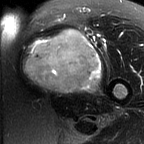
MRI of an extremity soft-tissue mass, one axial slice. T2-weighted fat-saturated. MR volume resampled by the dataset authors to the PET/CT grid (not the native acquisition matrix). 3.27 mm slice thickness. 144 × 144 image matrix. Female patient. From the clinical record (not read from this slice): histological type: pleiomorphic leiomyosarcoma; grade: intermediate; site of the primary tumour: left thigh.
Annotated regions visible in this slice (expert contour drawn on MRI and transferred to this co-registered scan by the dataset authors):
- gross tumour volume including surrounding oedema: box from (x=22, y=28) to (x=103, y=93) px
- gross tumour volume (mass): (x=22, y=28)–(x=103, y=93)